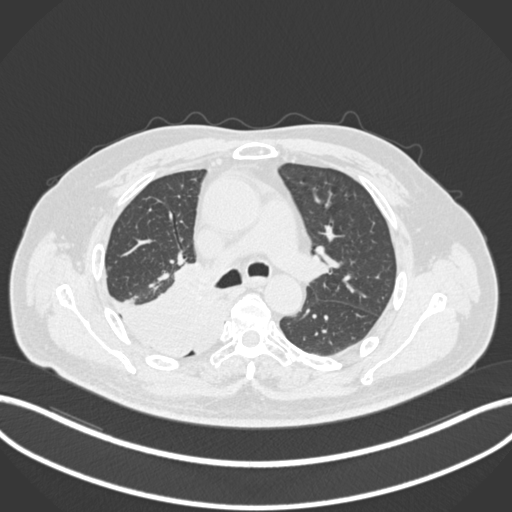
Chest CT, one axial slice. Position 128 of 218 along the scan axis. Lung window (W 1500 / L -600 HU). 512 × 512 image matrix. Patient: male, 68 years. From the clinical record (not read from this slice): clinical TNM (as recorded): T2a N0 M0.
Structures marked on this image (rectangle marked by the reading radiologist):
- lung tumour (recorded histology: adenocarcinoma): bounding box <108,265,227,359> (left, top, right, bottom; pixels)